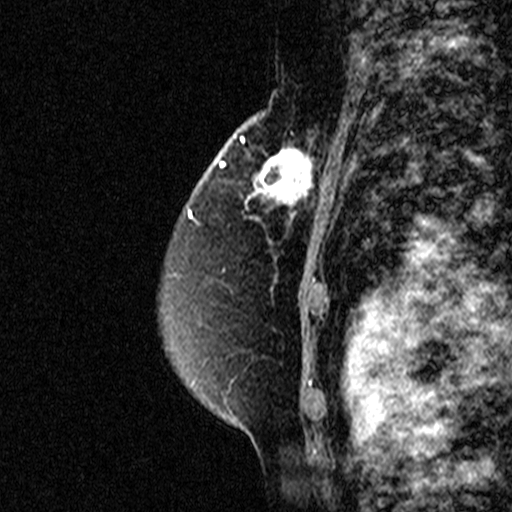
Breast MRI (dynamic contrast-enhanced), one sagittal slice. Dynamic contrast-enhanced study with each time point stored as its own series, time point 2 of 3 at this slice position (early post-contrast, ordered by acquisition time). 1.5 T. TE 4.5 ms, TR 11 ms. 3 mm slice thickness. 512 × 512 image matrix, field of view 200 × 200 mm. Female patient, age 49 years. From the clinical record (not read from this slice): setting: breast cancer imaged before/during neoadjuvant chemotherapy; receptor status: triple-negative.
Outlined on this slice (semi-automatically segmented with operator editing):
- analysis volume of interest (the breast-tissue region the enhancement analysis was run in; not a lesion): box from (x=250, y=122) to (x=331, y=227) px
- tumour enhancement mask (voxels above the 90 % enhancement threshold inside the analysis volume of interest): (x=253, y=146)–(x=315, y=217)